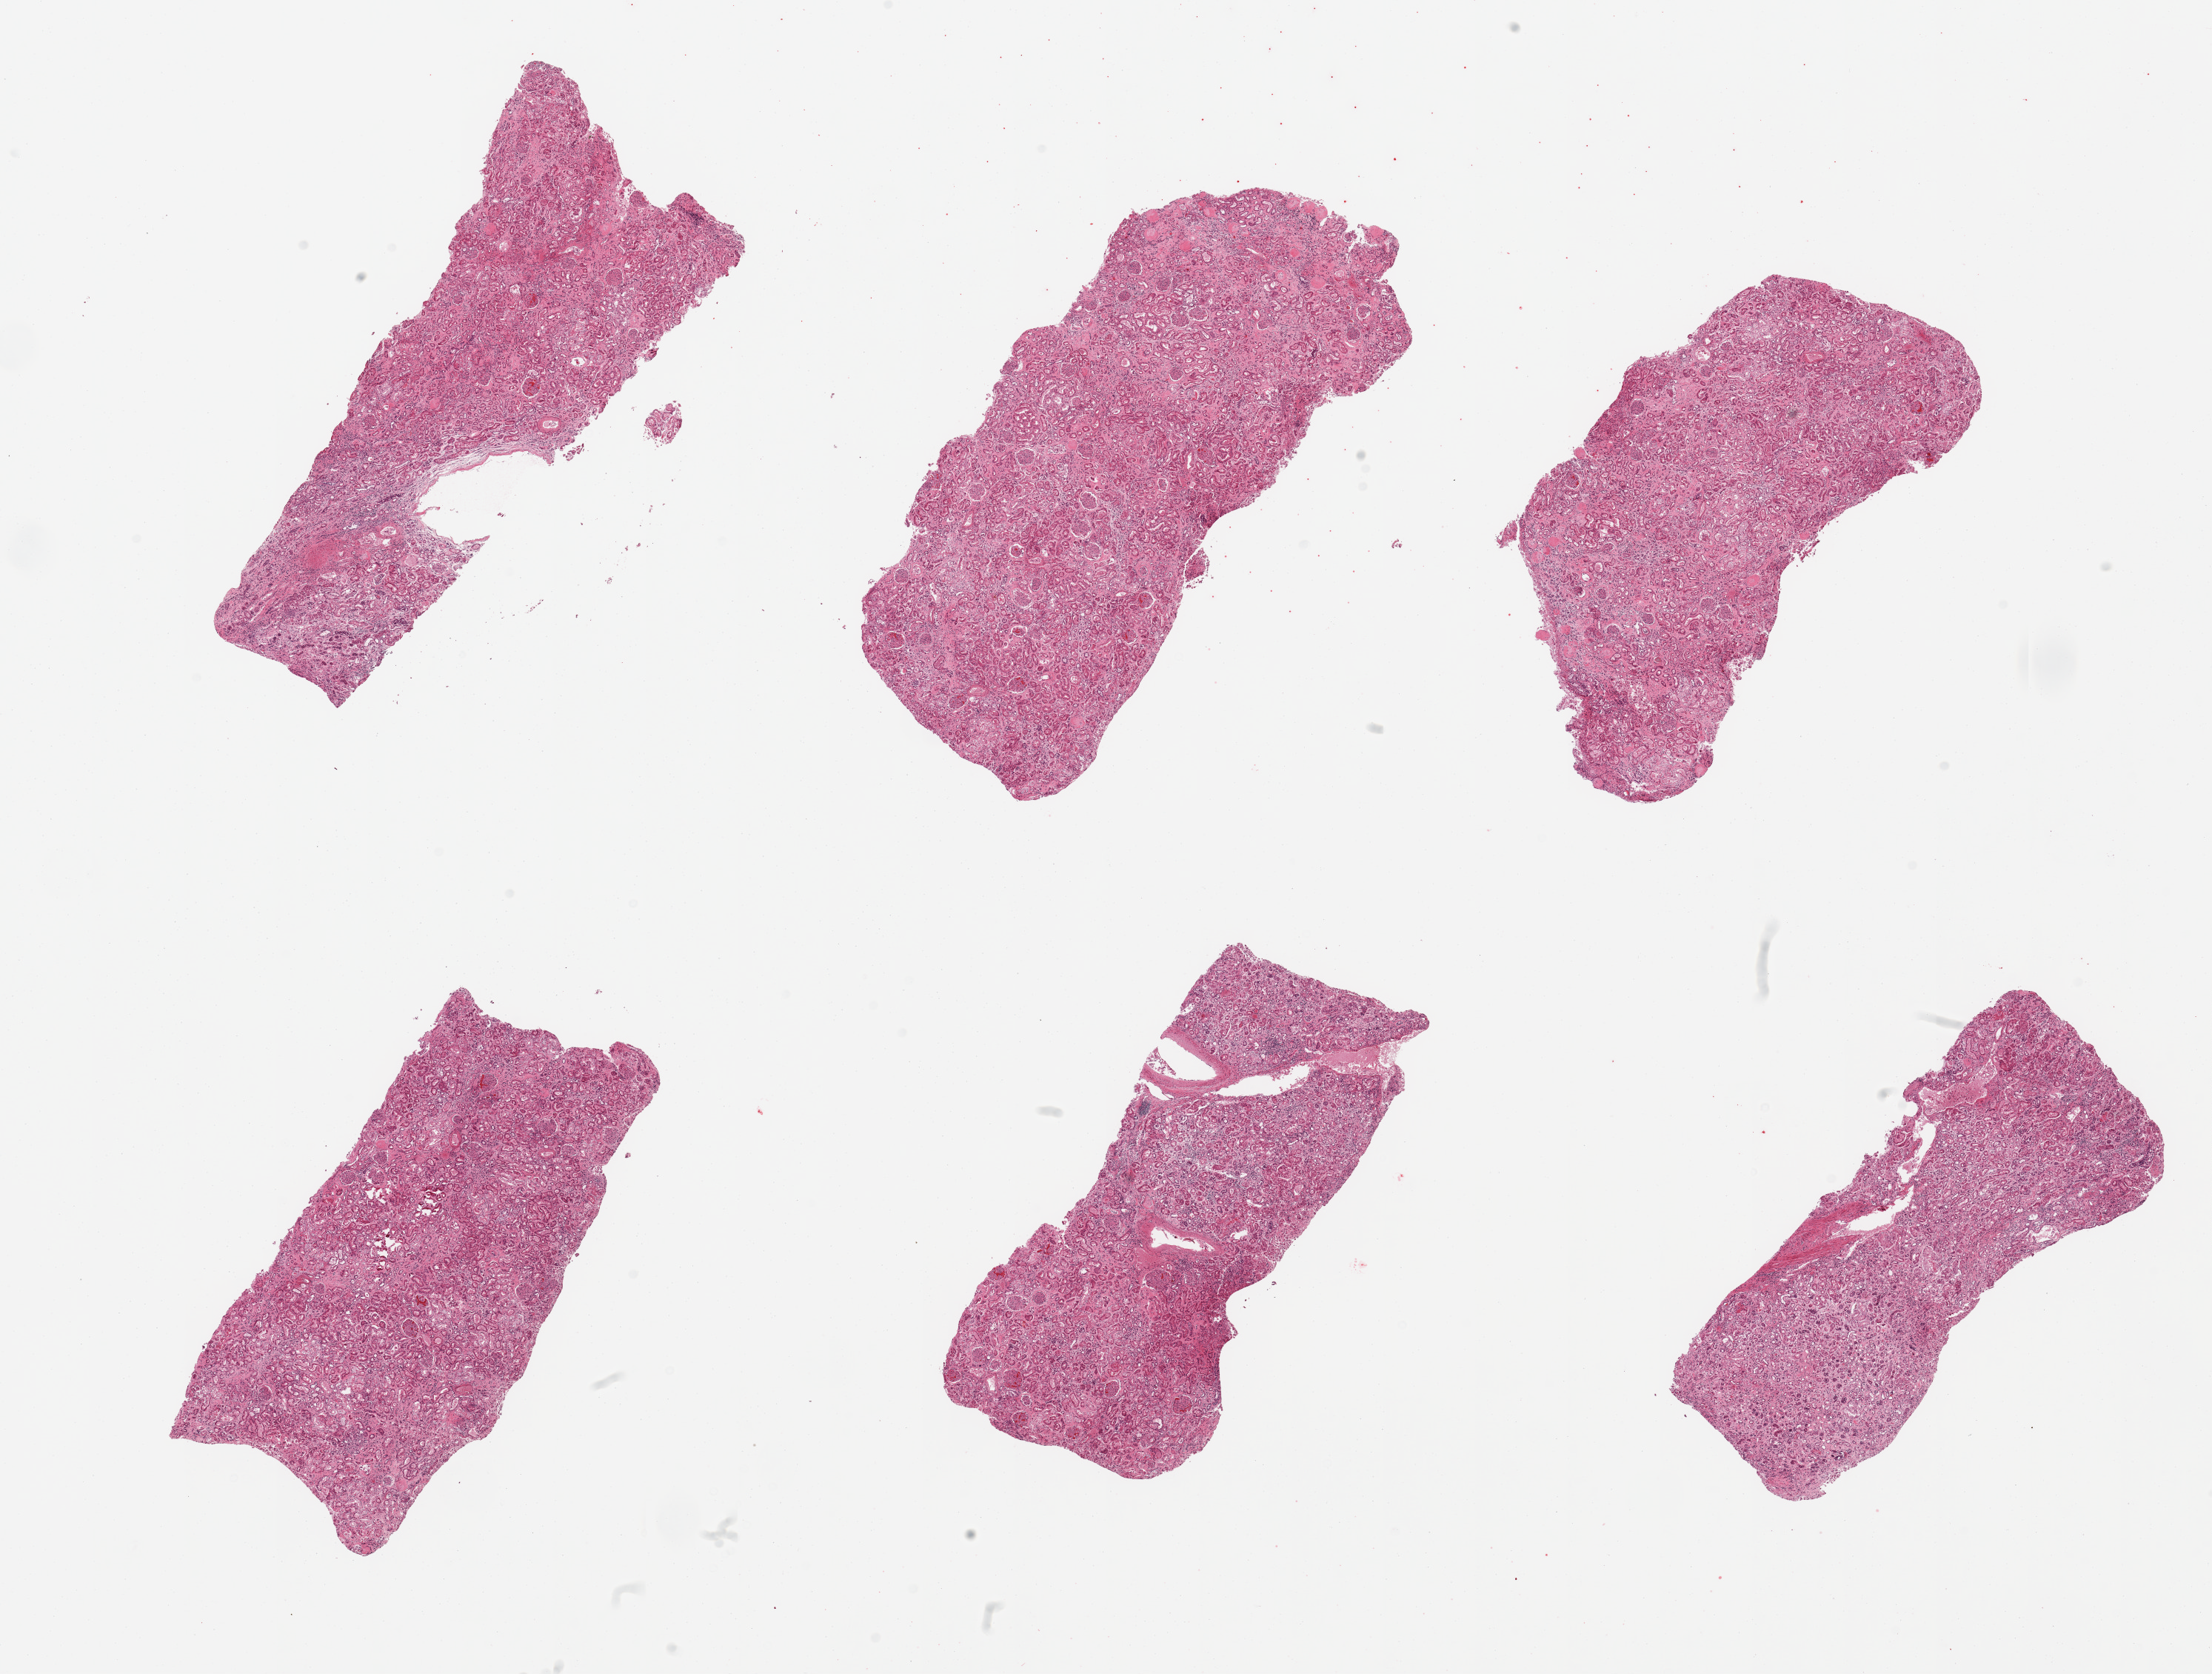
Haematoxylin and eosin whole-slide image, brightfield — shown as a low-resolution overview of the whole scanned area (about 23.6 x 17.9 mm, acquisition: 20x scan); PAXgene-fixed, paraffin-embedded tissue; target tissue: renal cortex; donor tissue sample. Female donor.
Review note (as recorded): 6 pieces; 1 piece is medulla; fibrin thrombi in glomeruli; focal scarring; tubules vacuolated.